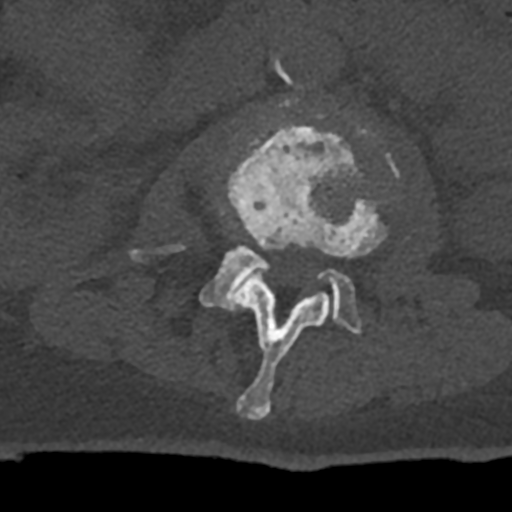
CT including the spine, one axial slice; position 353 of 797 along the scan axis; bone window (W 1800 / L 400 HU); 0.5 mm slice thickness; 512 × 512 image matrix, field of view 160 × 160 mm. Male patient, age 74 years. From the clinical record (not read from this slice): primary cancer: renal; vertebrae with lytic lesions (as recorded): T10, L1, L2, L3, L4, L5.
Structures marked on this image (semi-automatically segmented with operator editing):
- L2 vertebra: bounding box <218,123,386,420> (left, top, right, bottom; pixels)
- L3 vertebra: <130,99,361,334>